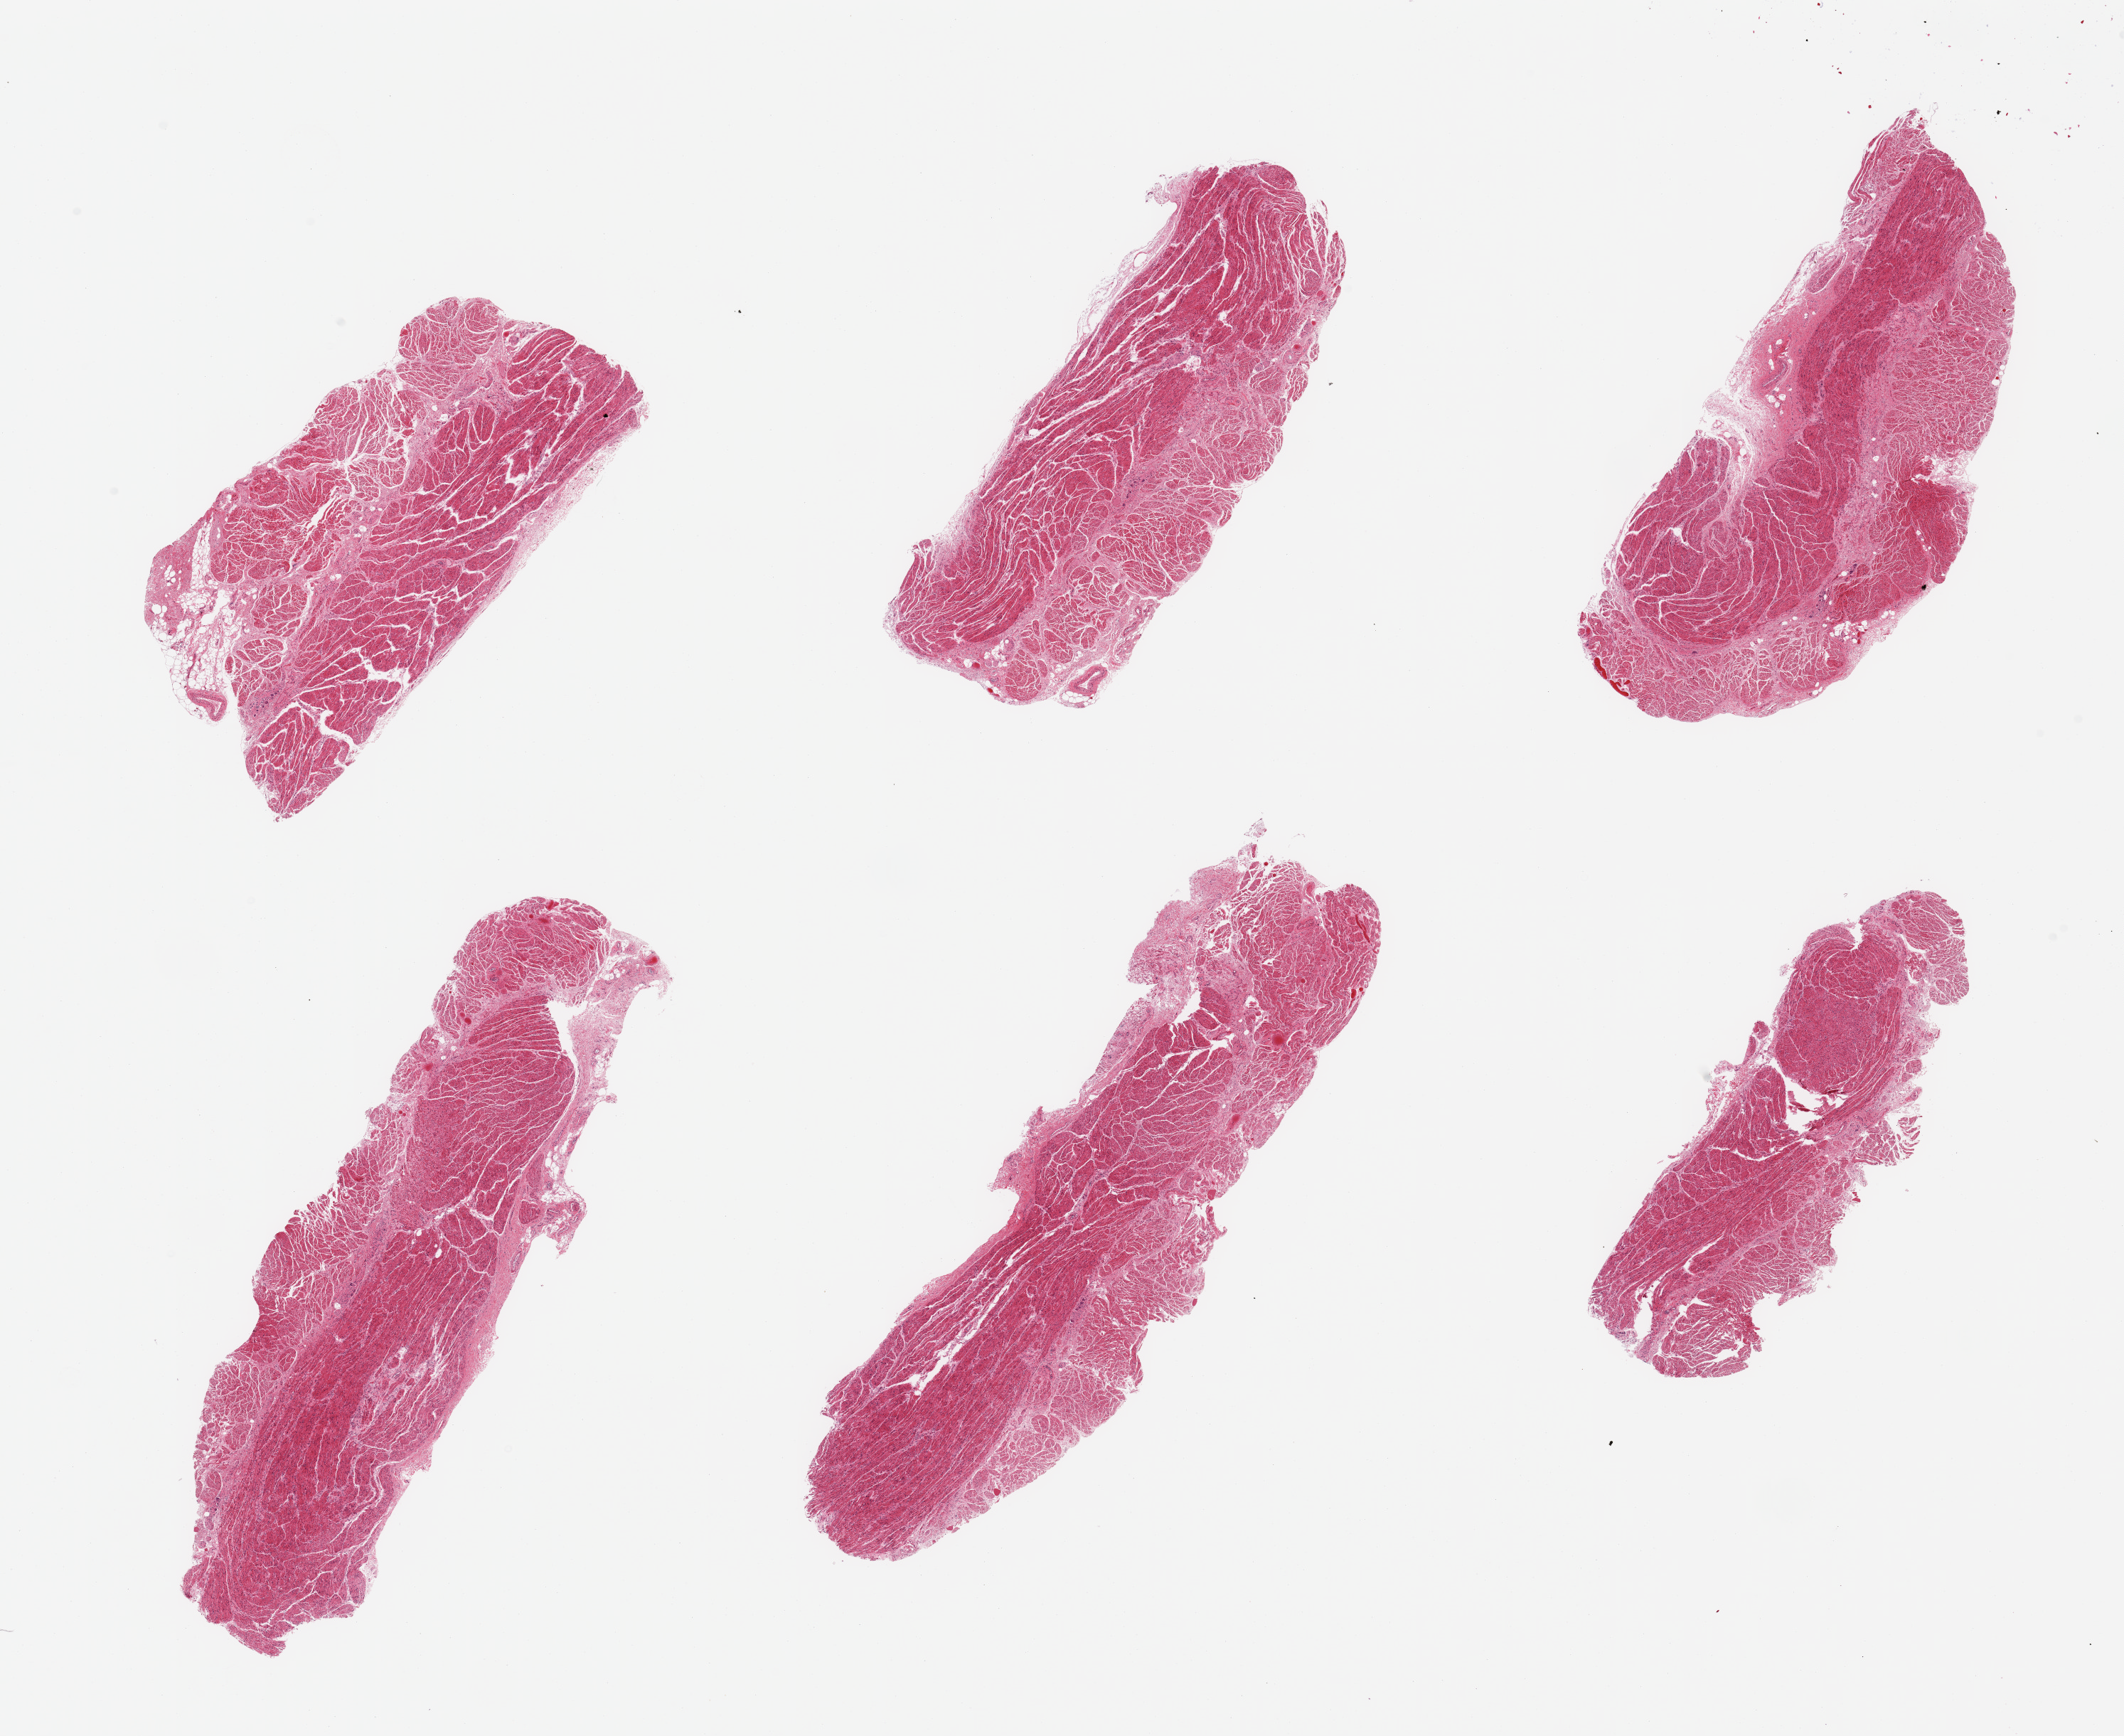
Digitized haematoxylin and eosin-stained section, low-resolution overview of the scanned area, about 23.6 x 19.3 mm. PAXgene-fixed, paraffin-embedded tissue. Target tissue: gastroesophageal junction. Donor tissue sample. Male donor.
Review note (as recorded): 6 pieces, confirmed target muscularis.